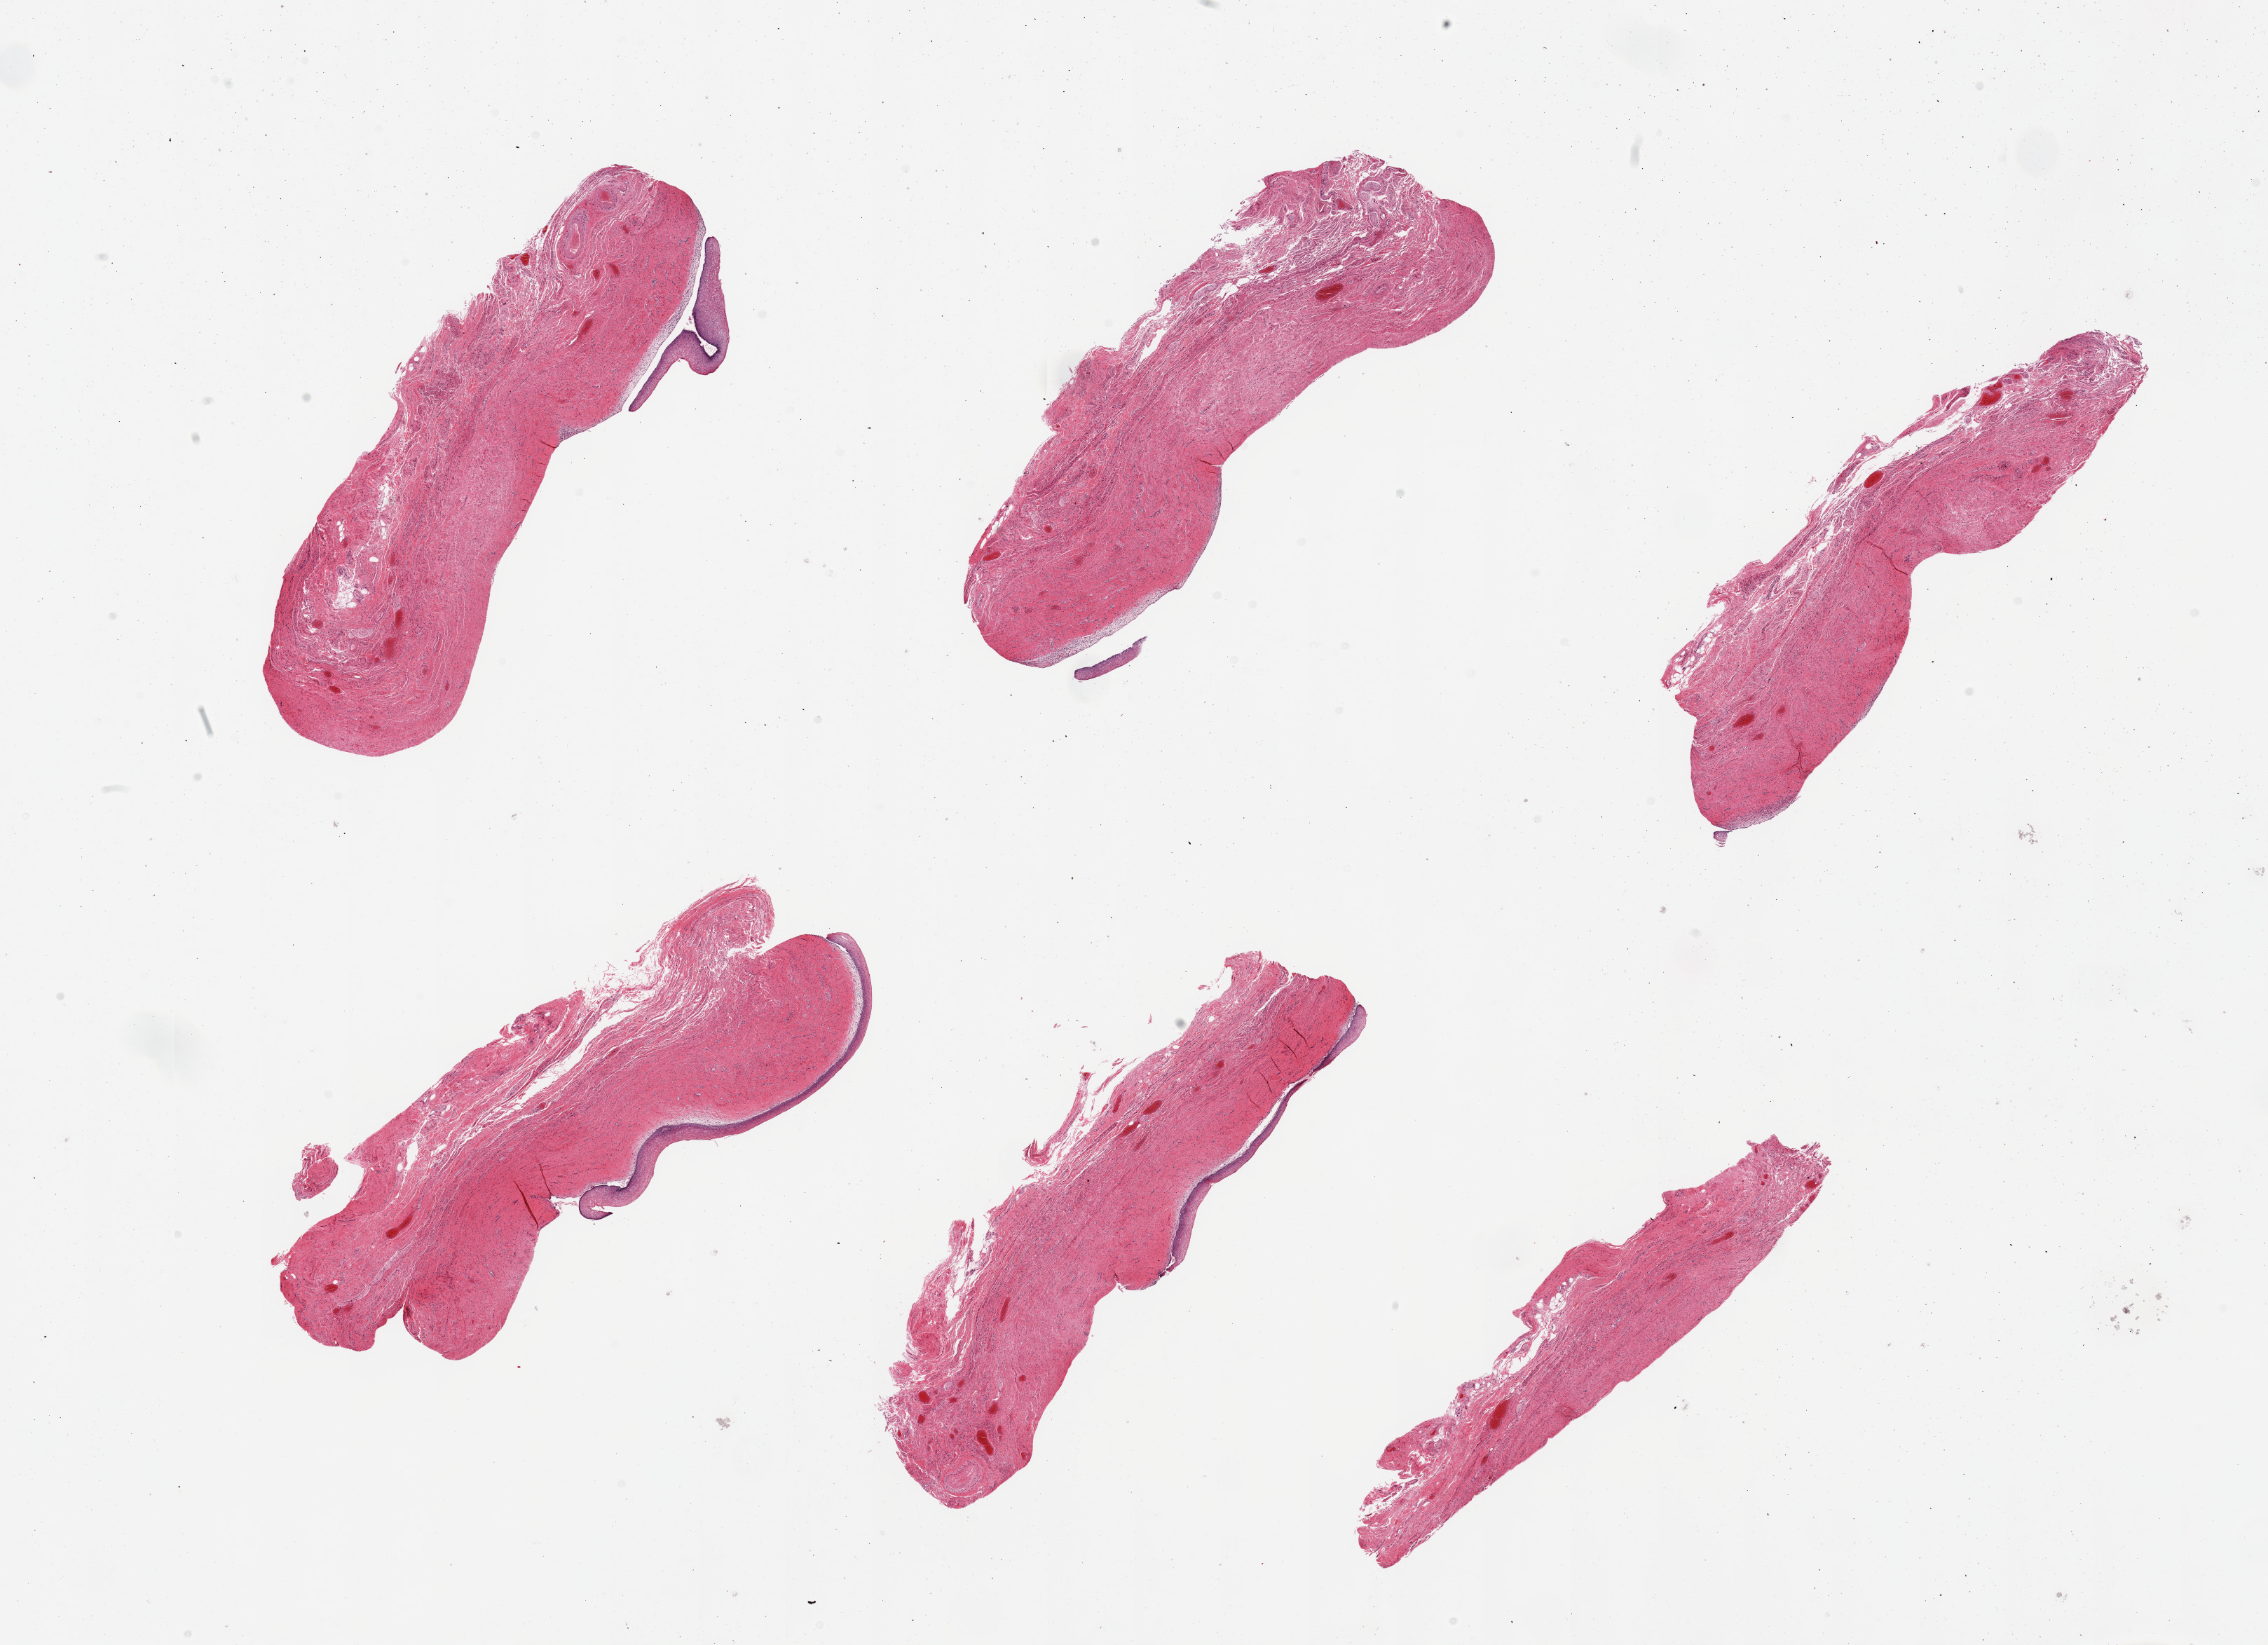
Haematoxylin and eosin whole-slide image — whole scanned area (about 25.6 x 18.6 mm, acquisition: 20x scan) shown as a low-resolution overview; PAXgene-fixed paraffin-embedded (PFPE) section; section of vagina (target tissue); tissue donor sample. Donor: female.
- review note (as recorded): 6 pieces; epithelium largely detached or sloughed